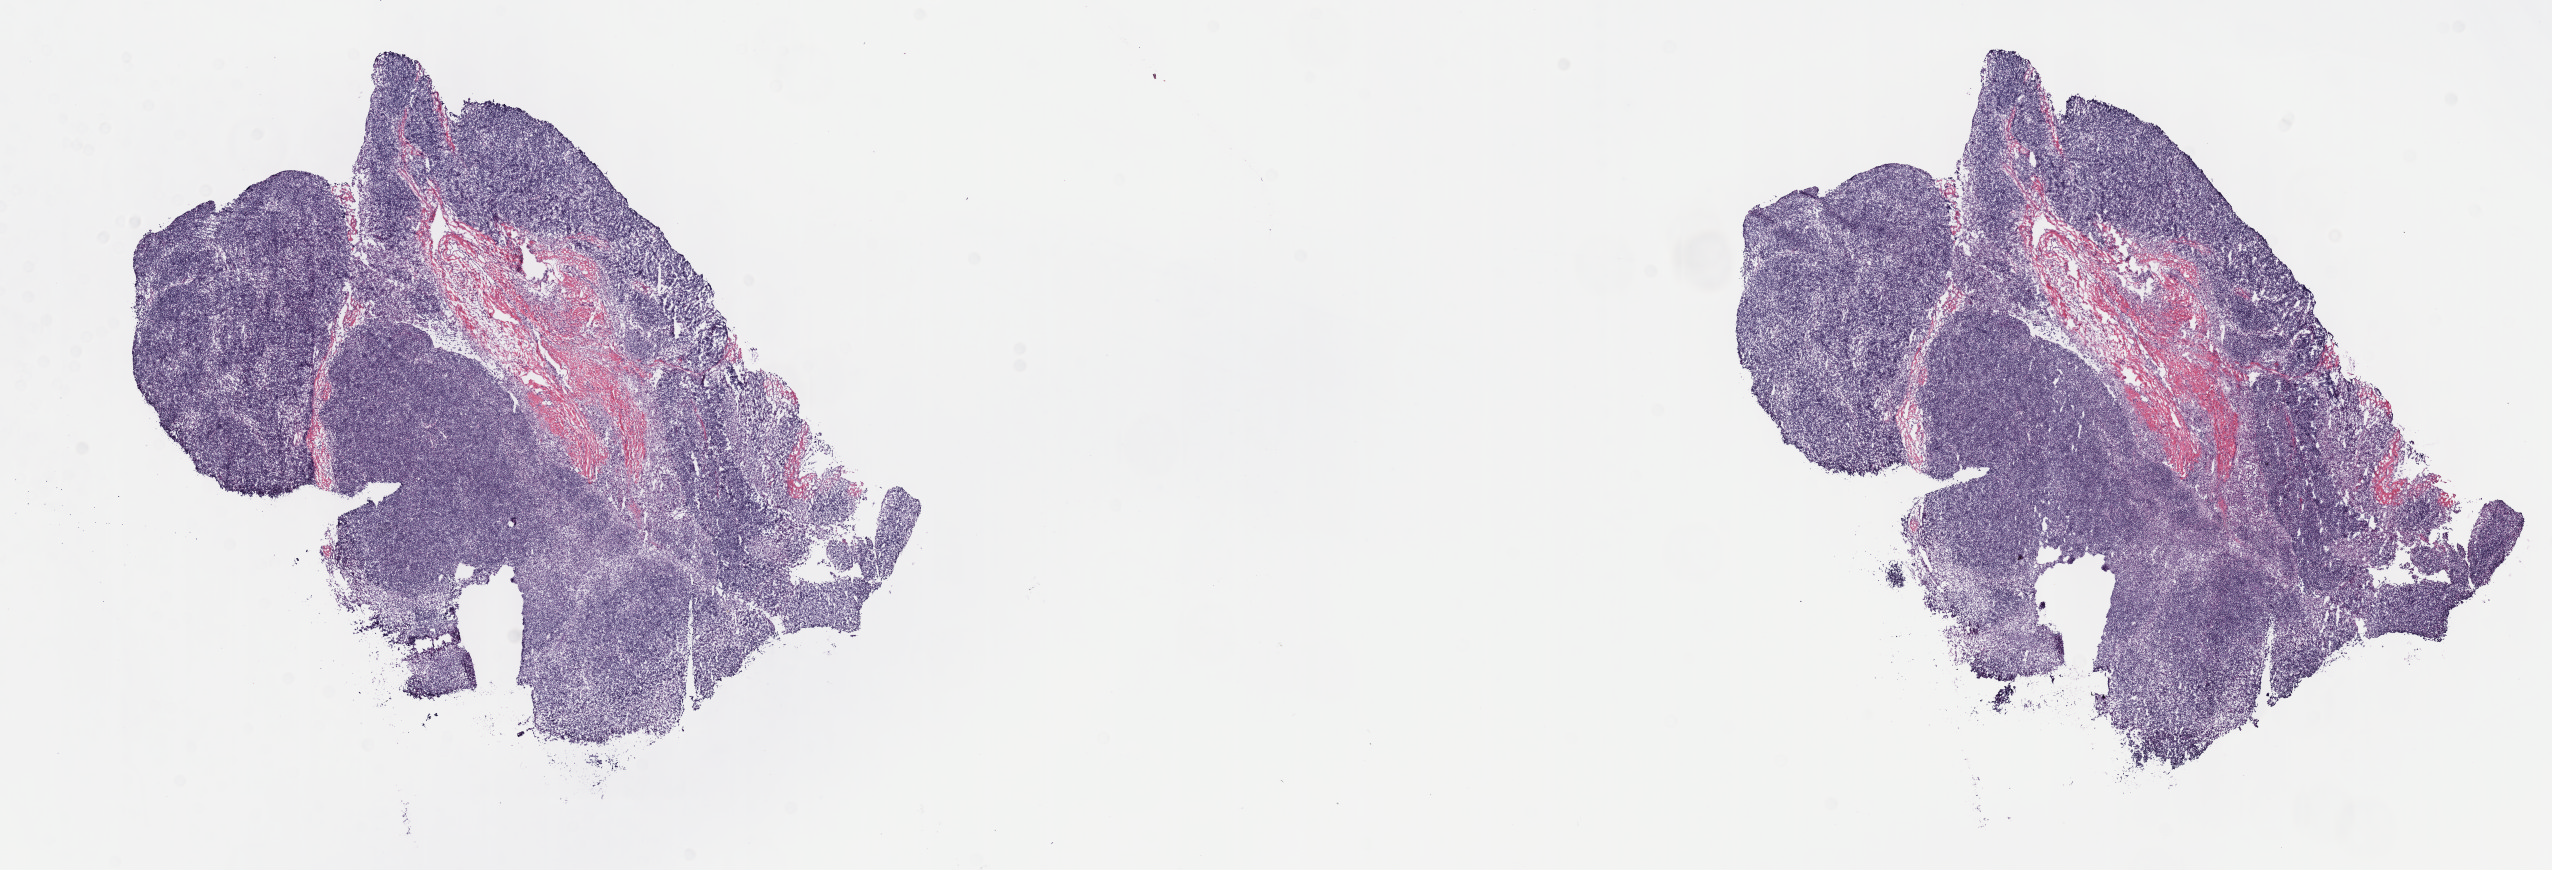
H&E whole-slide image, a low-resolution overview of the entire scanned area, about 20.6 x 7.0 mm (from a 40x scan). Frozen section. Sample: primary tumour, thymus. Female, age 52 years at initial diagnosis. Pathologist review of this section (percent, as recorded): tumour cells 85%, tumour nuclei 95%.
Histologic diagnosis: Thymoma, type AB, malignant (anterior mediastinum).